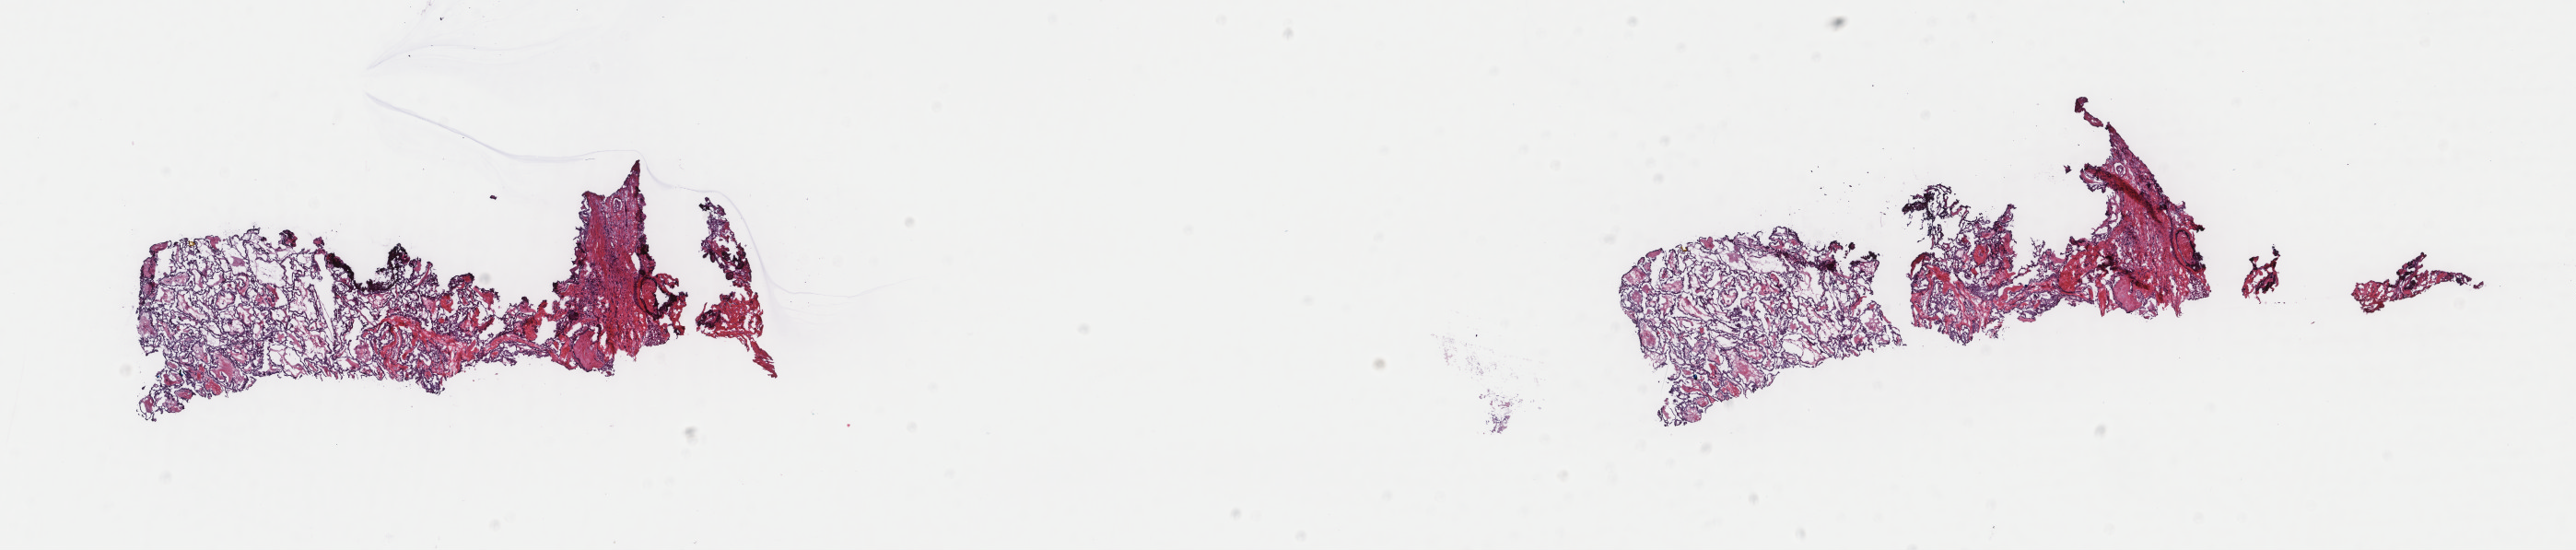
Whole-slide histology image, H&E, shown as a low-resolution overview of the whole scanned area (about 22.2 x 4.7 mm, acquisition: 40x scan), frozen section from the top of the tissue portion, primary tumour sample from the thyroid. Male, age 20 years at initial diagnosis. Slide review estimates, as recorded: tumour cells 80%, tumour nuclei 100%, normal cells 0%, stromal cells 20%, necrosis 0%. Inflammatory infiltration, as recorded: lymphocyte infiltration 1%, monocyte infiltration 2%, neutrophil infiltration 1%.
• lymph nodes positive (case pathology): 1 of 4 examined
• histologic diagnosis: Papillary adenocarcinoma, NOS (thyroid gland)
• laterality: bilateral
• TNM: T2 N1 MX
• AJCC pathologic stage: I